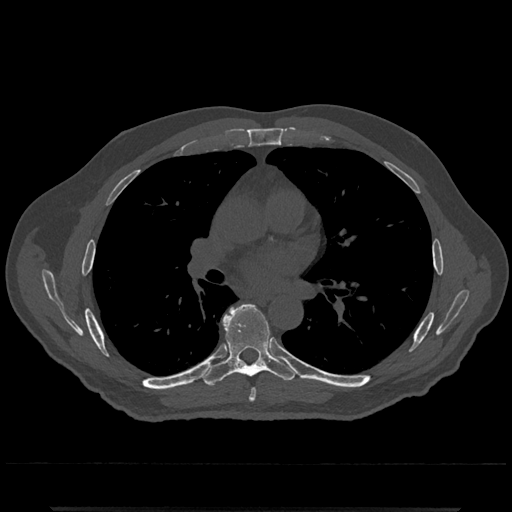
CT including the spine, one axial slice; slice 733 of 797 in the series (ordered by position); 120 kVp; bone window (W 1800 / L 400 HU); 0.5 mm slice thickness; 512 × 512 image matrix. Patient: male, 67 years. Case-level facts recorded for this patient, not image findings: primary cancer: prostate.
Outlined on this slice (semi-automatically segmented with operator editing):
- T6 vertebra: bounding box [x1, y1, x2, y2] px = [249, 389, 256, 402]
- T7 vertebra: [203, 304, 297, 386]